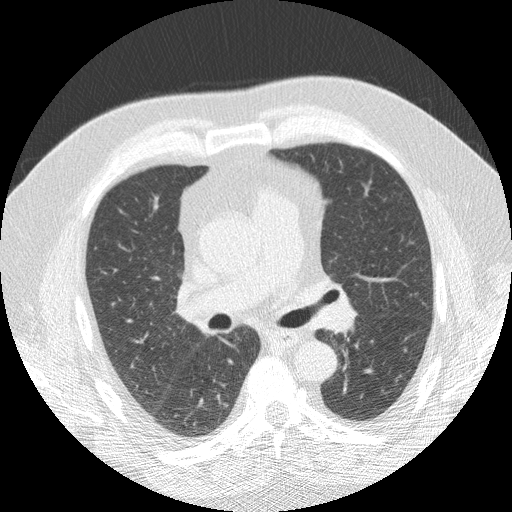
Chest CT (low-dose screening protocol), one axial image; baseline screening round; lung window (W 1500 / L -600 HU); slice 65 of 166 in the series; 512 × 512 image matrix. Male participant, aged 69 years at enrolment. Former smoker at enrolment.
Expert reader's lesion annotation, bounding box (x1, y1, x2, y2) in pixels: (369, 370, 402, 409). Screening reader's record for this exam: no non-calcified nodule ≥4 mm recorded. Official screen result: negative screen, minor abnormalities not suspicious for lung cancer. Participant outcome: lung cancer diagnosed 939 days after this screen — squamous cell carcinoma, NOS, left lower lobe, moderately differentiated (G2), stage IA (AJCC 6th edition), 14 mm at pathology.